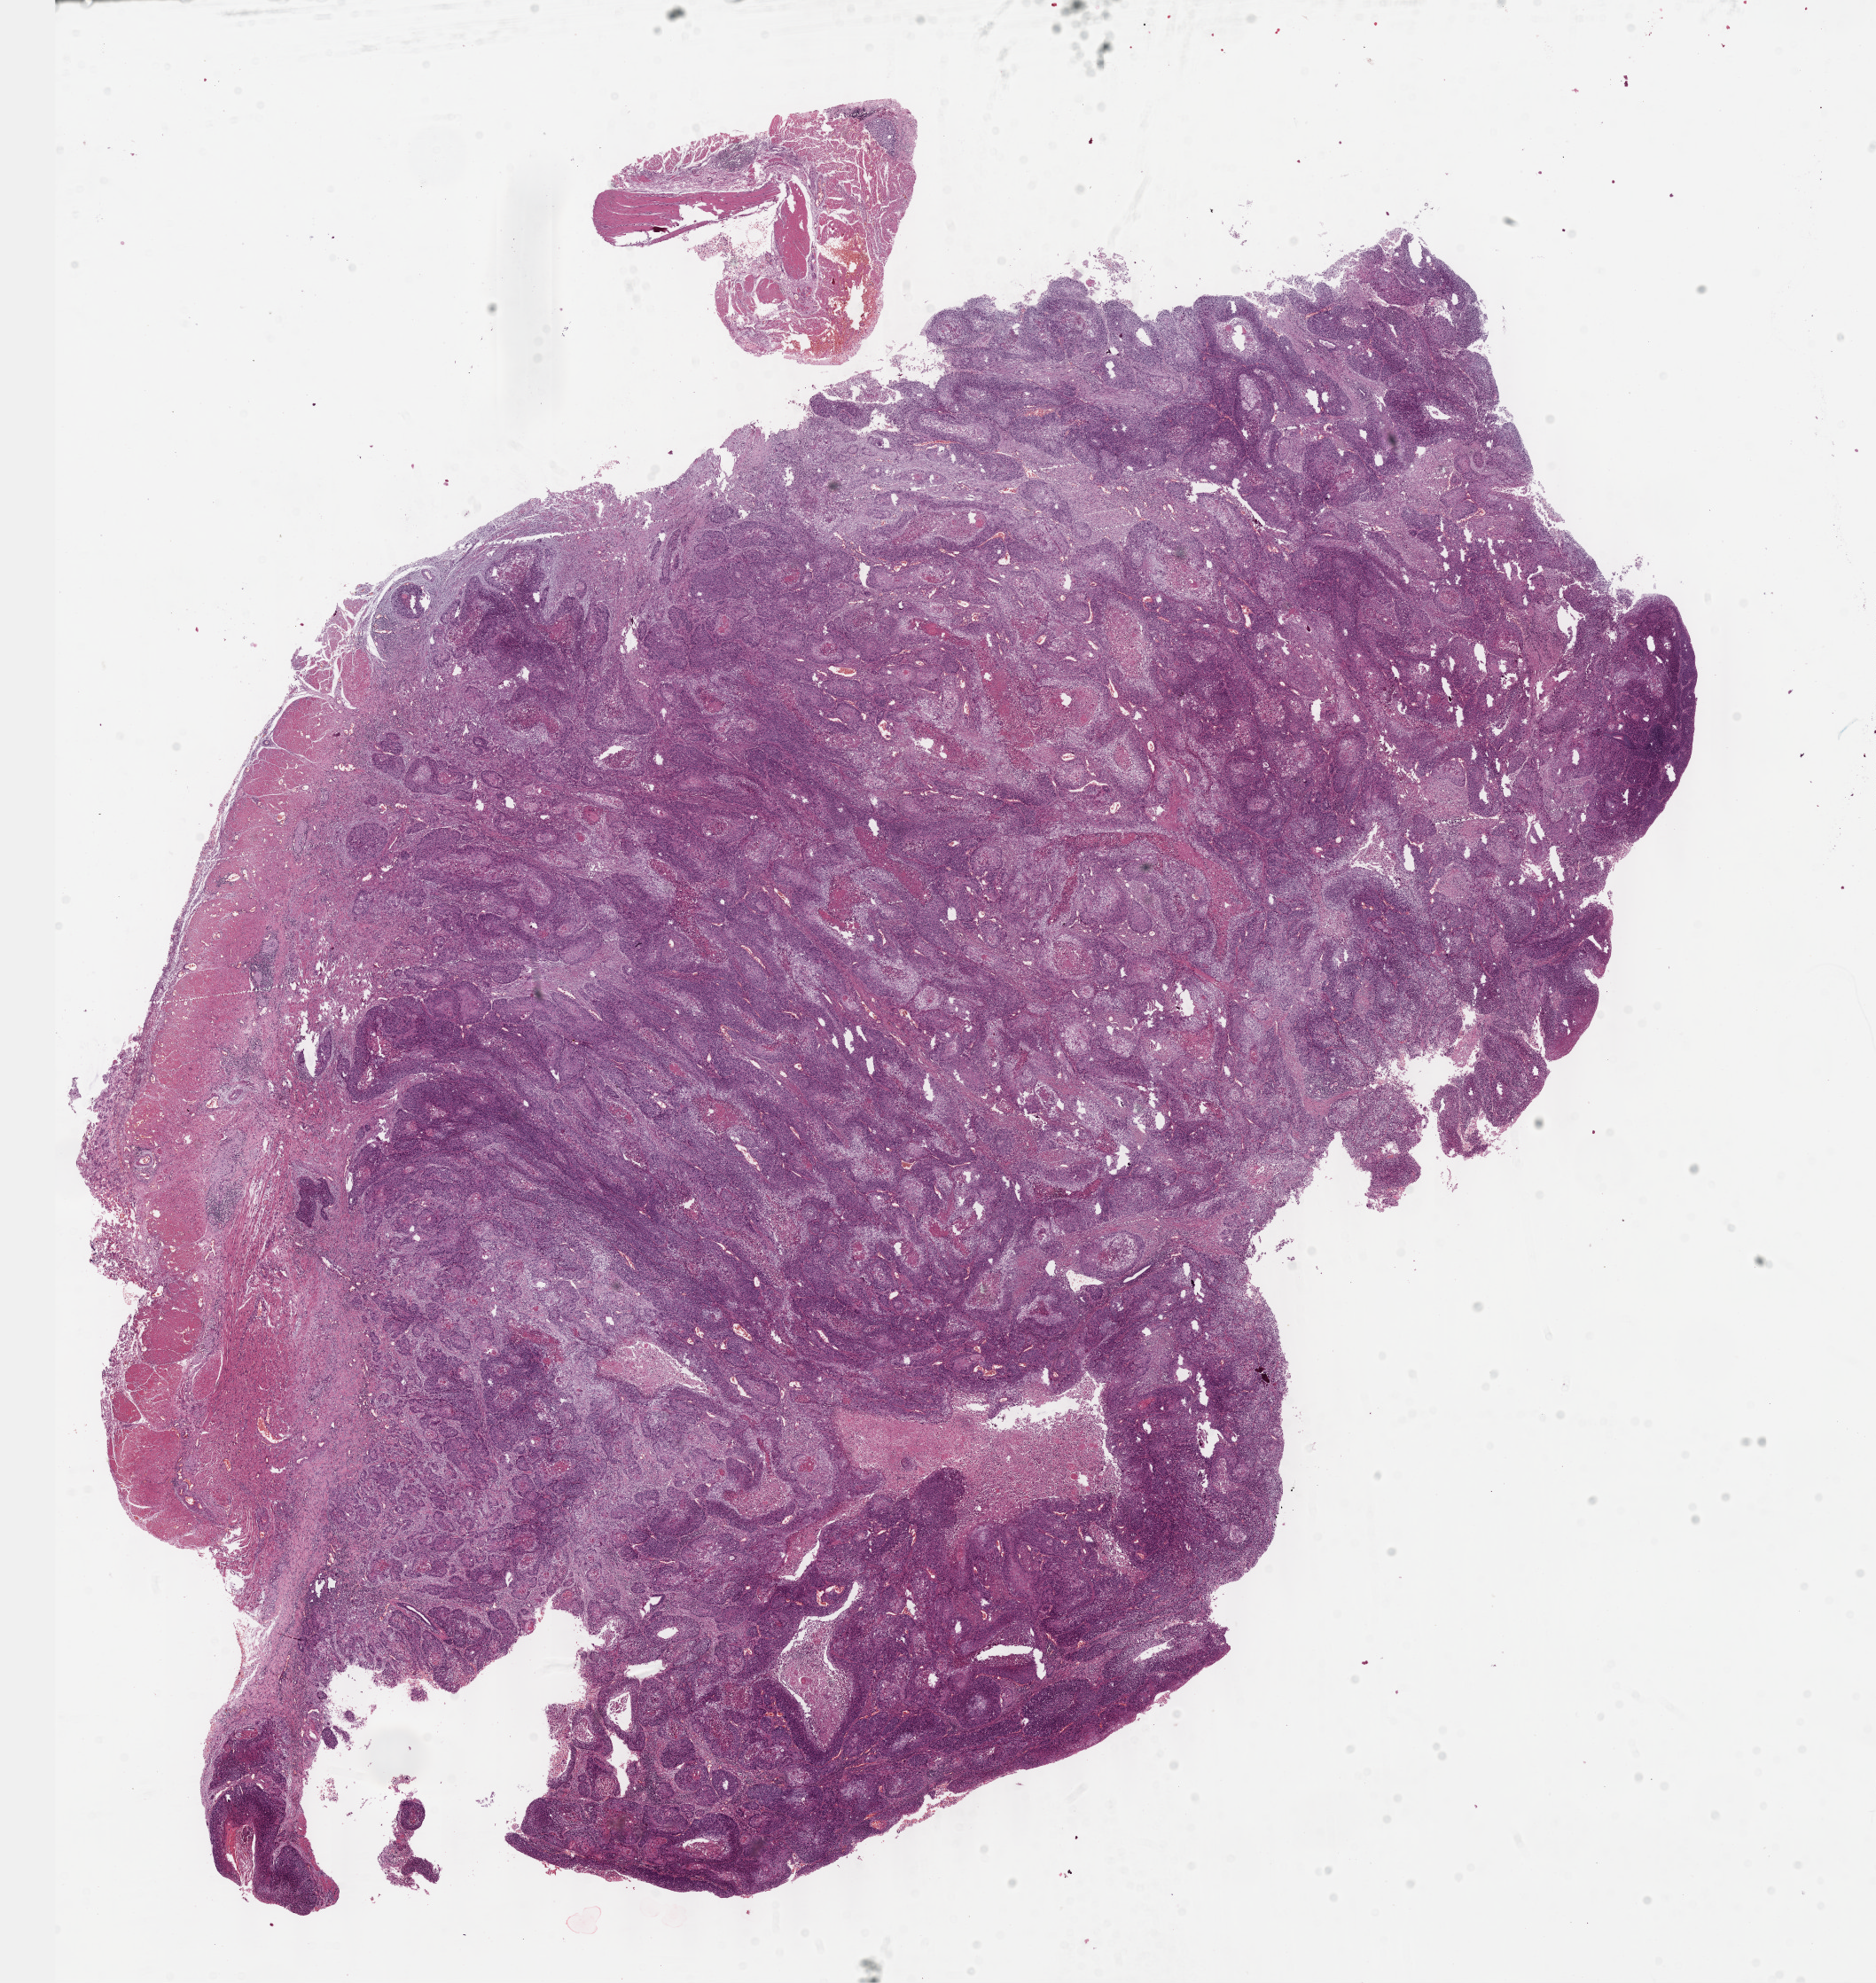
Hematoxylin and eosin (H&E) stained whole-slide image — whole scanned area (about 17.1 x 18.1 mm, slide scanned at 40x) shown as a low-resolution overview, formalin-fixed paraffin-embedded (FFPE) diagnostic section, sample: primary tumour, esophagus. Male, age 72 years at initial diagnosis. Histologic grade: G2 (moderately differentiated).
- AJCC pathologic stage: IIA (6th edition)
- pathologic diagnosis: Squamous cell carcinoma, NOS